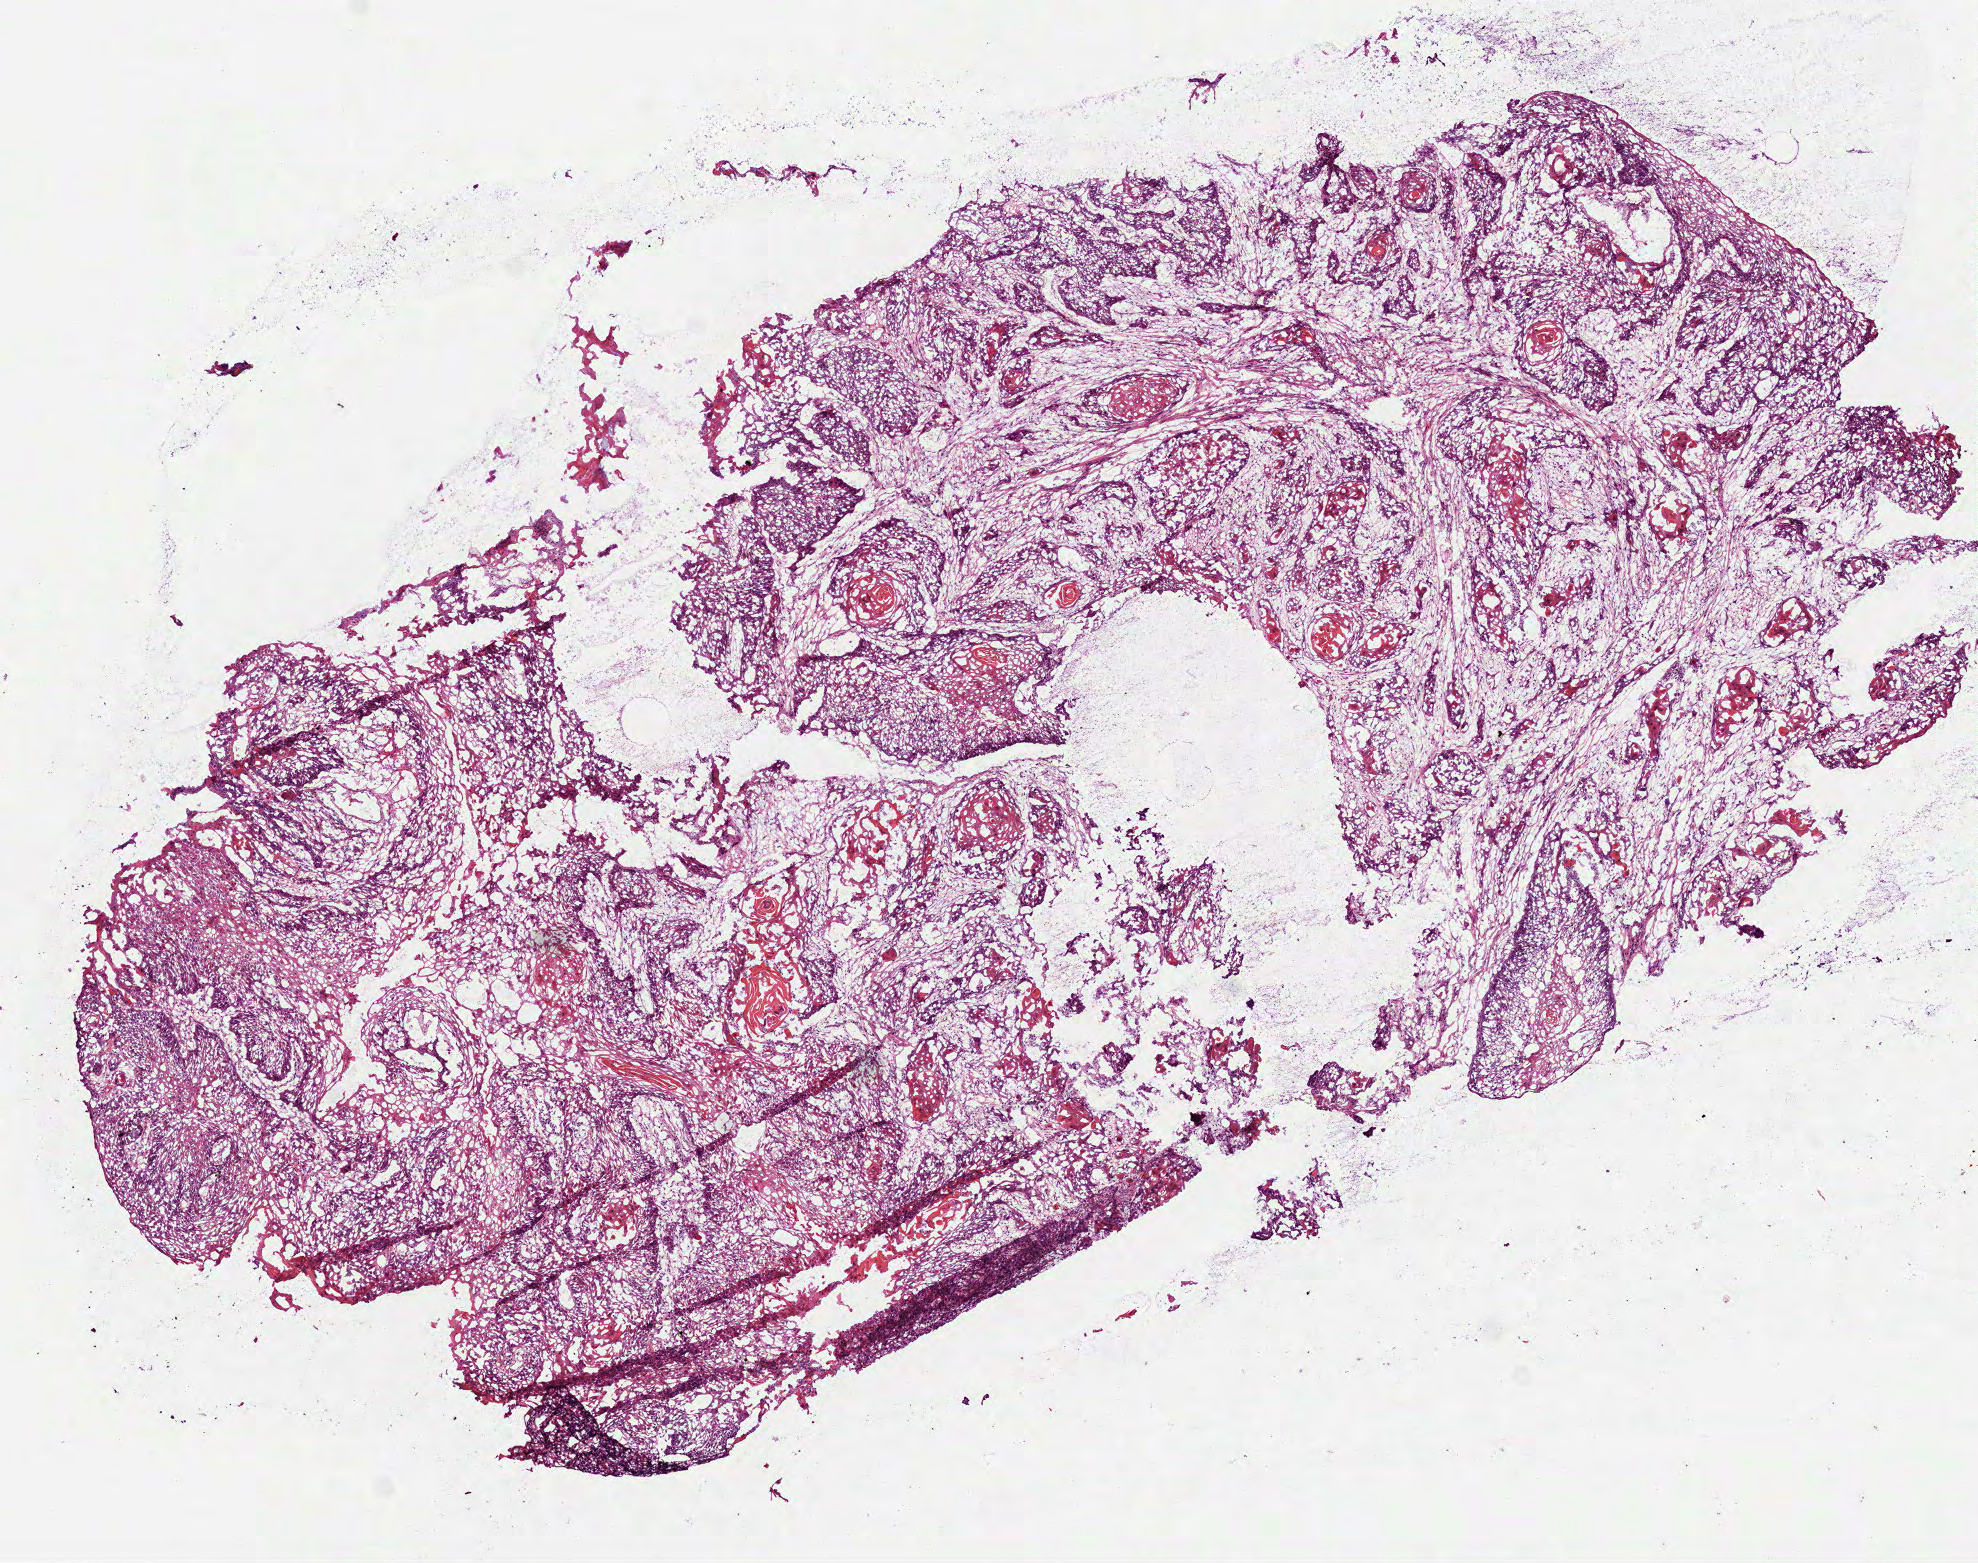
H&E-stained whole-slide image, shown as a low-resolution overview of the whole scanned area (about 8.0 x 6.3 mm, acquisition: 40x scan), frozen section from the top of the tissue portion, head and neck, primary tumour sample. Male patient; age at initial diagnosis 62 years. Composition of this section per pathologist review: tumour cells 70%, tumour nuclei 75%.
Diagnosis: Squamous cell carcinoma, NOS (larynx, NOS).